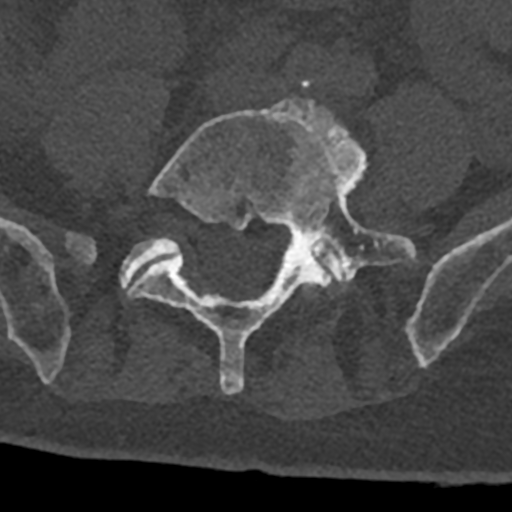
CT including the spine, one axial slice; slice 199 of 797 in the series (ordered by position); reconstruction kernel Br40s/3; bone window (W 1800 / L 400 HU); 0.5 mm slice thickness; 512 × 512 image matrix, field of view 160 × 160 mm. Patient: male, 74 years. From the clinical record (not read from this slice): primary cancer: renal; vertebrae with lytic lesions (as recorded): T10, L1, L2, L3, L4, L5.
Outlined on this slice (semi-automatic segmentation, software-assisted and operator-edited):
- L4 vertebra: bounding box <295,282,313,293> (left, top, right, bottom; pixels)
- L5 vertebra: <128,97,416,394>